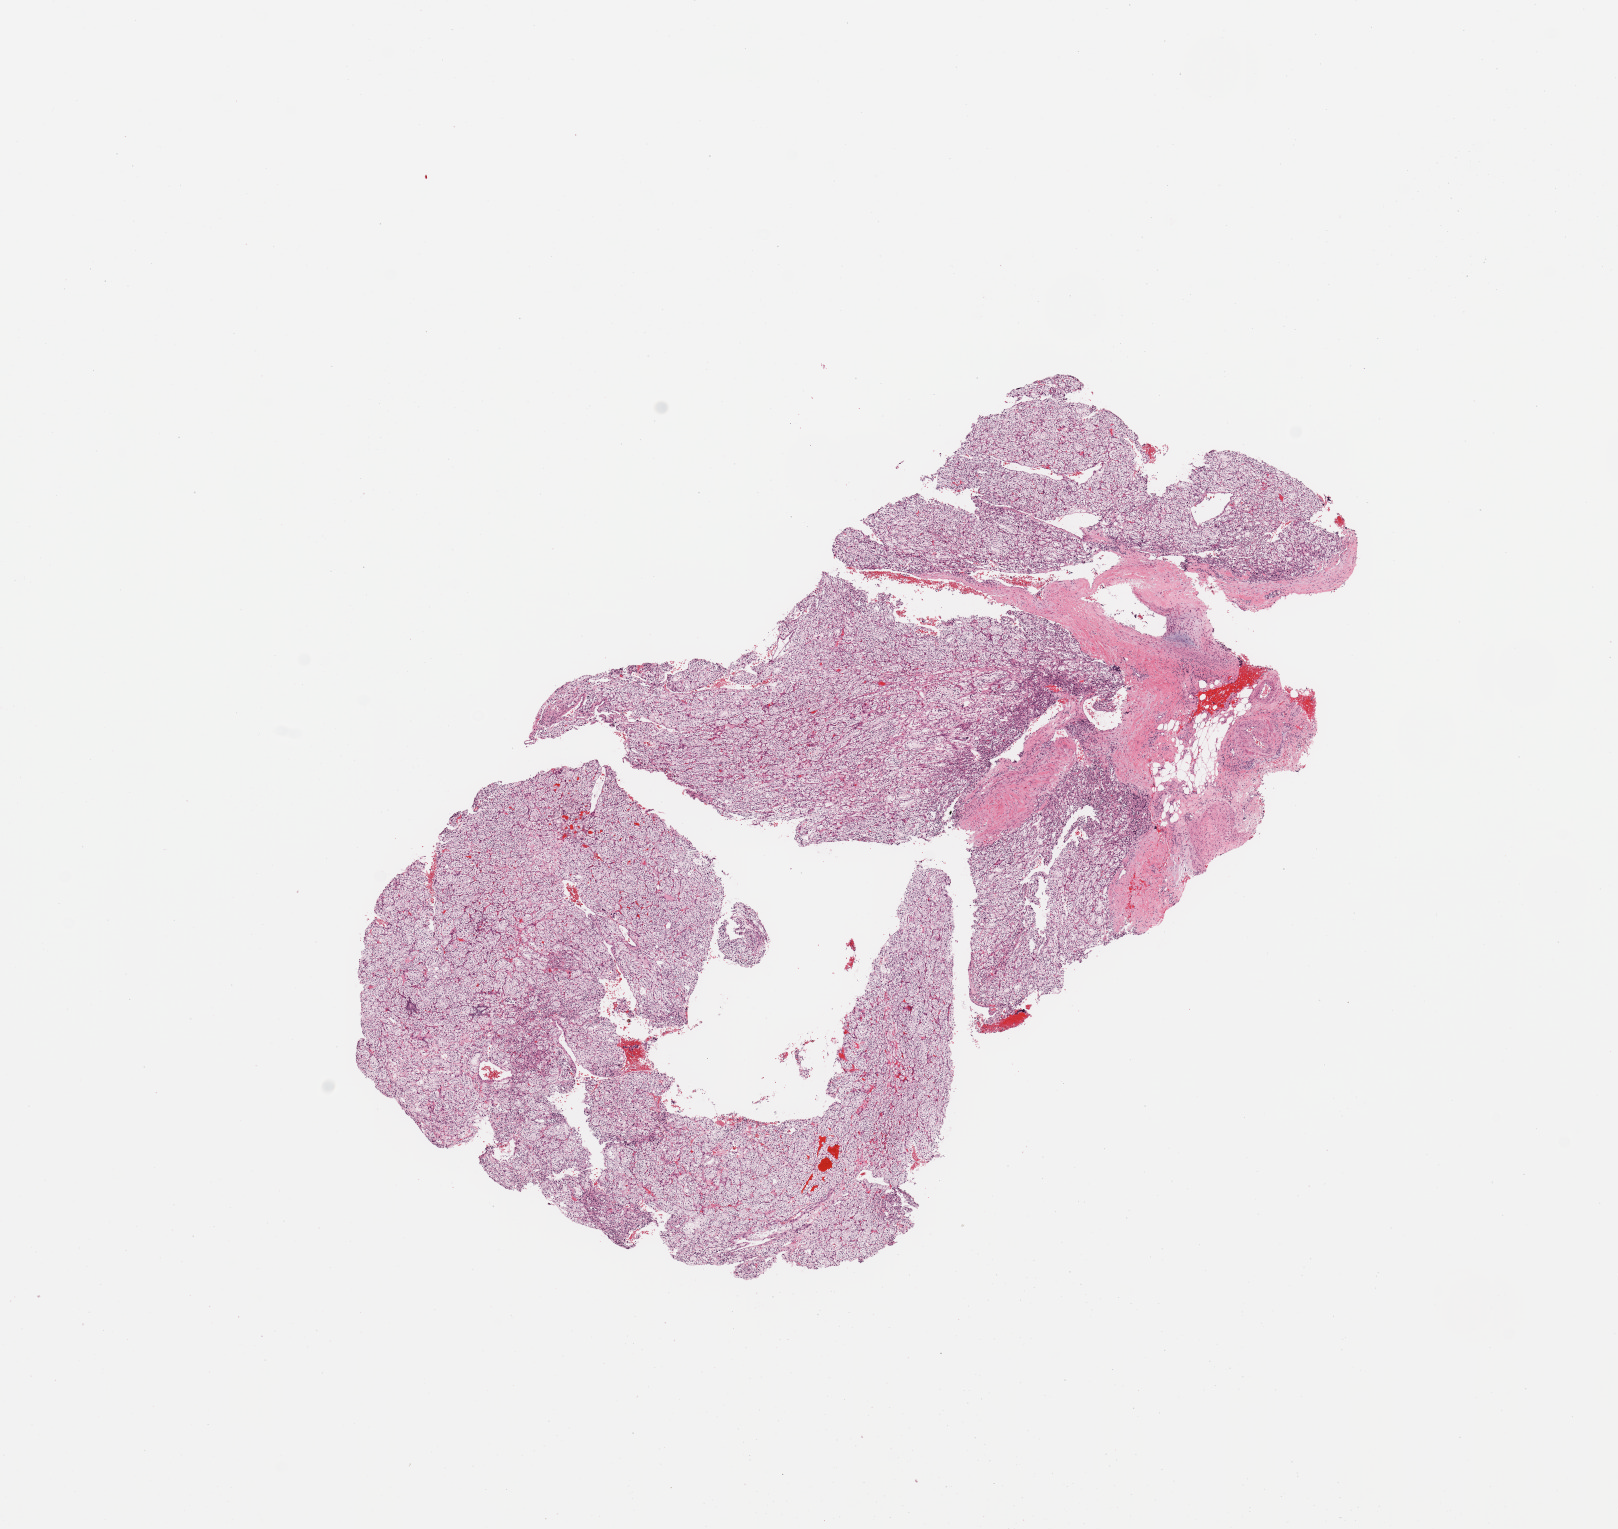
H&E whole-slide image, shown as a low-resolution overview of the whole scanned area (about 12.8 x 12.1 mm, acquisition: 20x scan); kidney, tumour tissue. 54-year-old female patient. Histologic grade: G2 (moderately differentiated).
Histologic diagnosis: Renal cell carcinoma, NOS. AJCC pathologic stage: III.